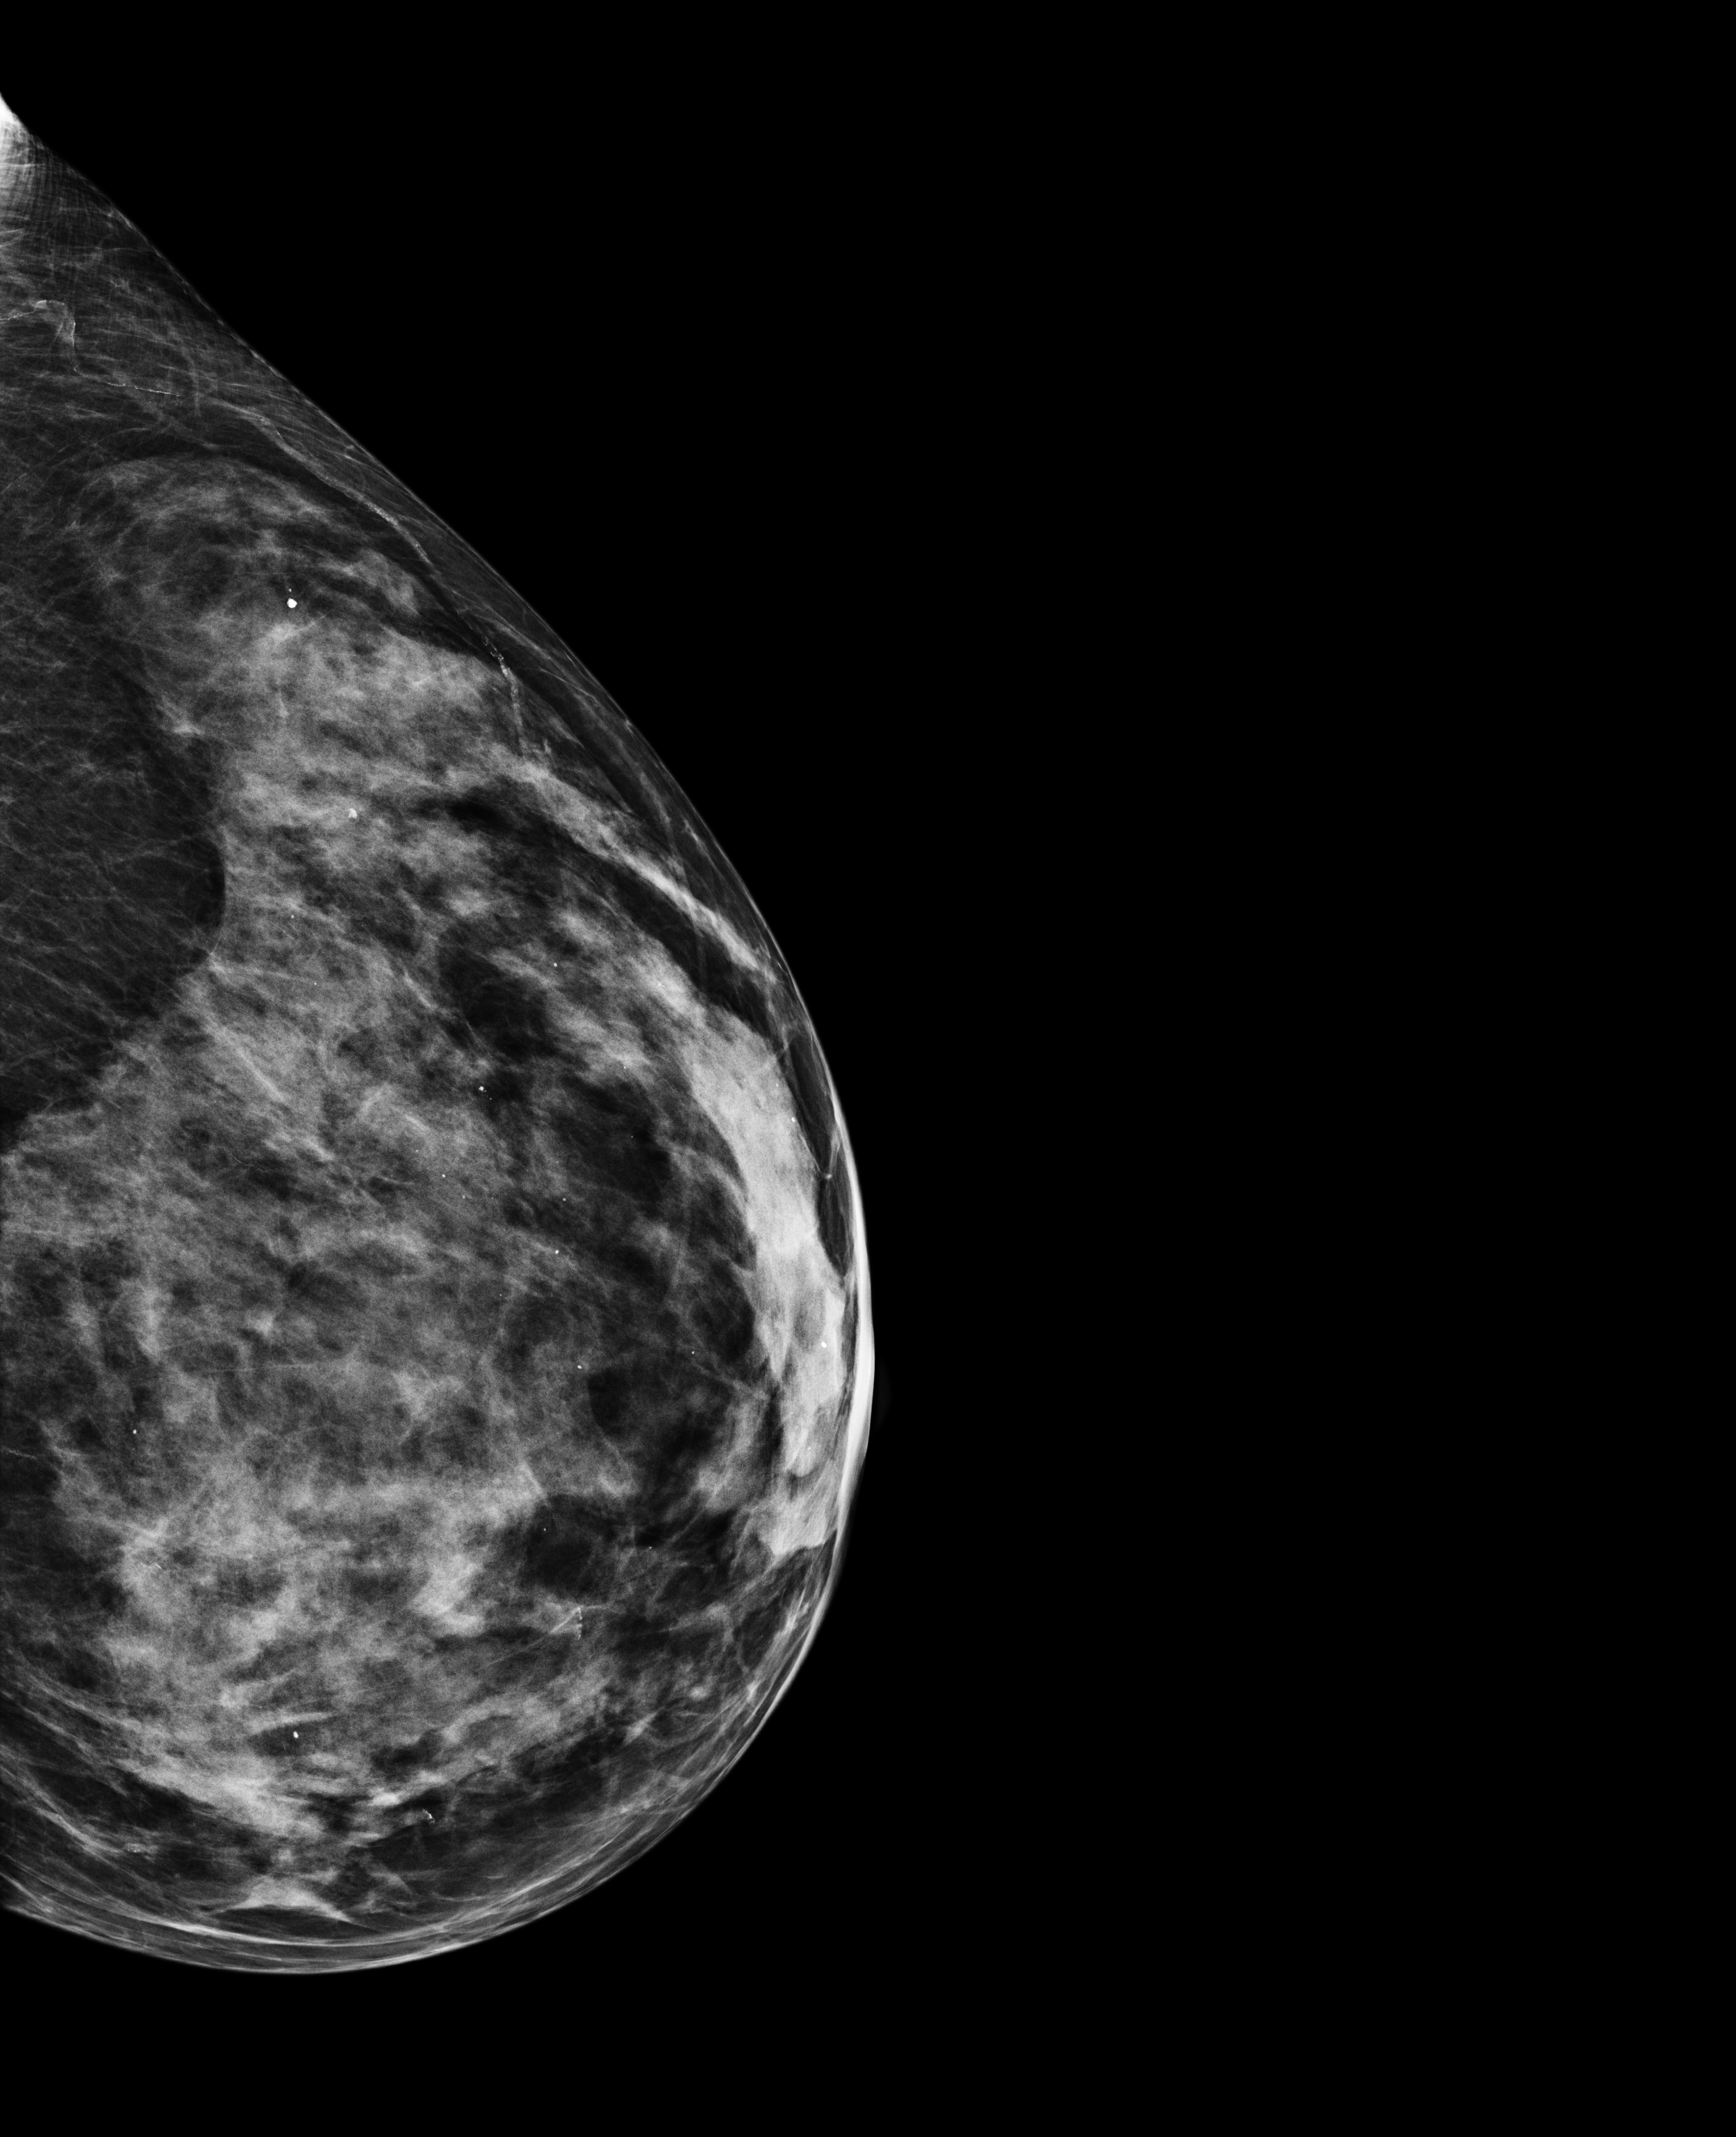
Screening examination; compressed breast thickness 44 mm; system: Selenia Dimensions. Patient: female, 75 years.
Image type: full-field digital mammogram. Breast: left. Projection: laterally exaggerated craniocaudal (XCCL) view.